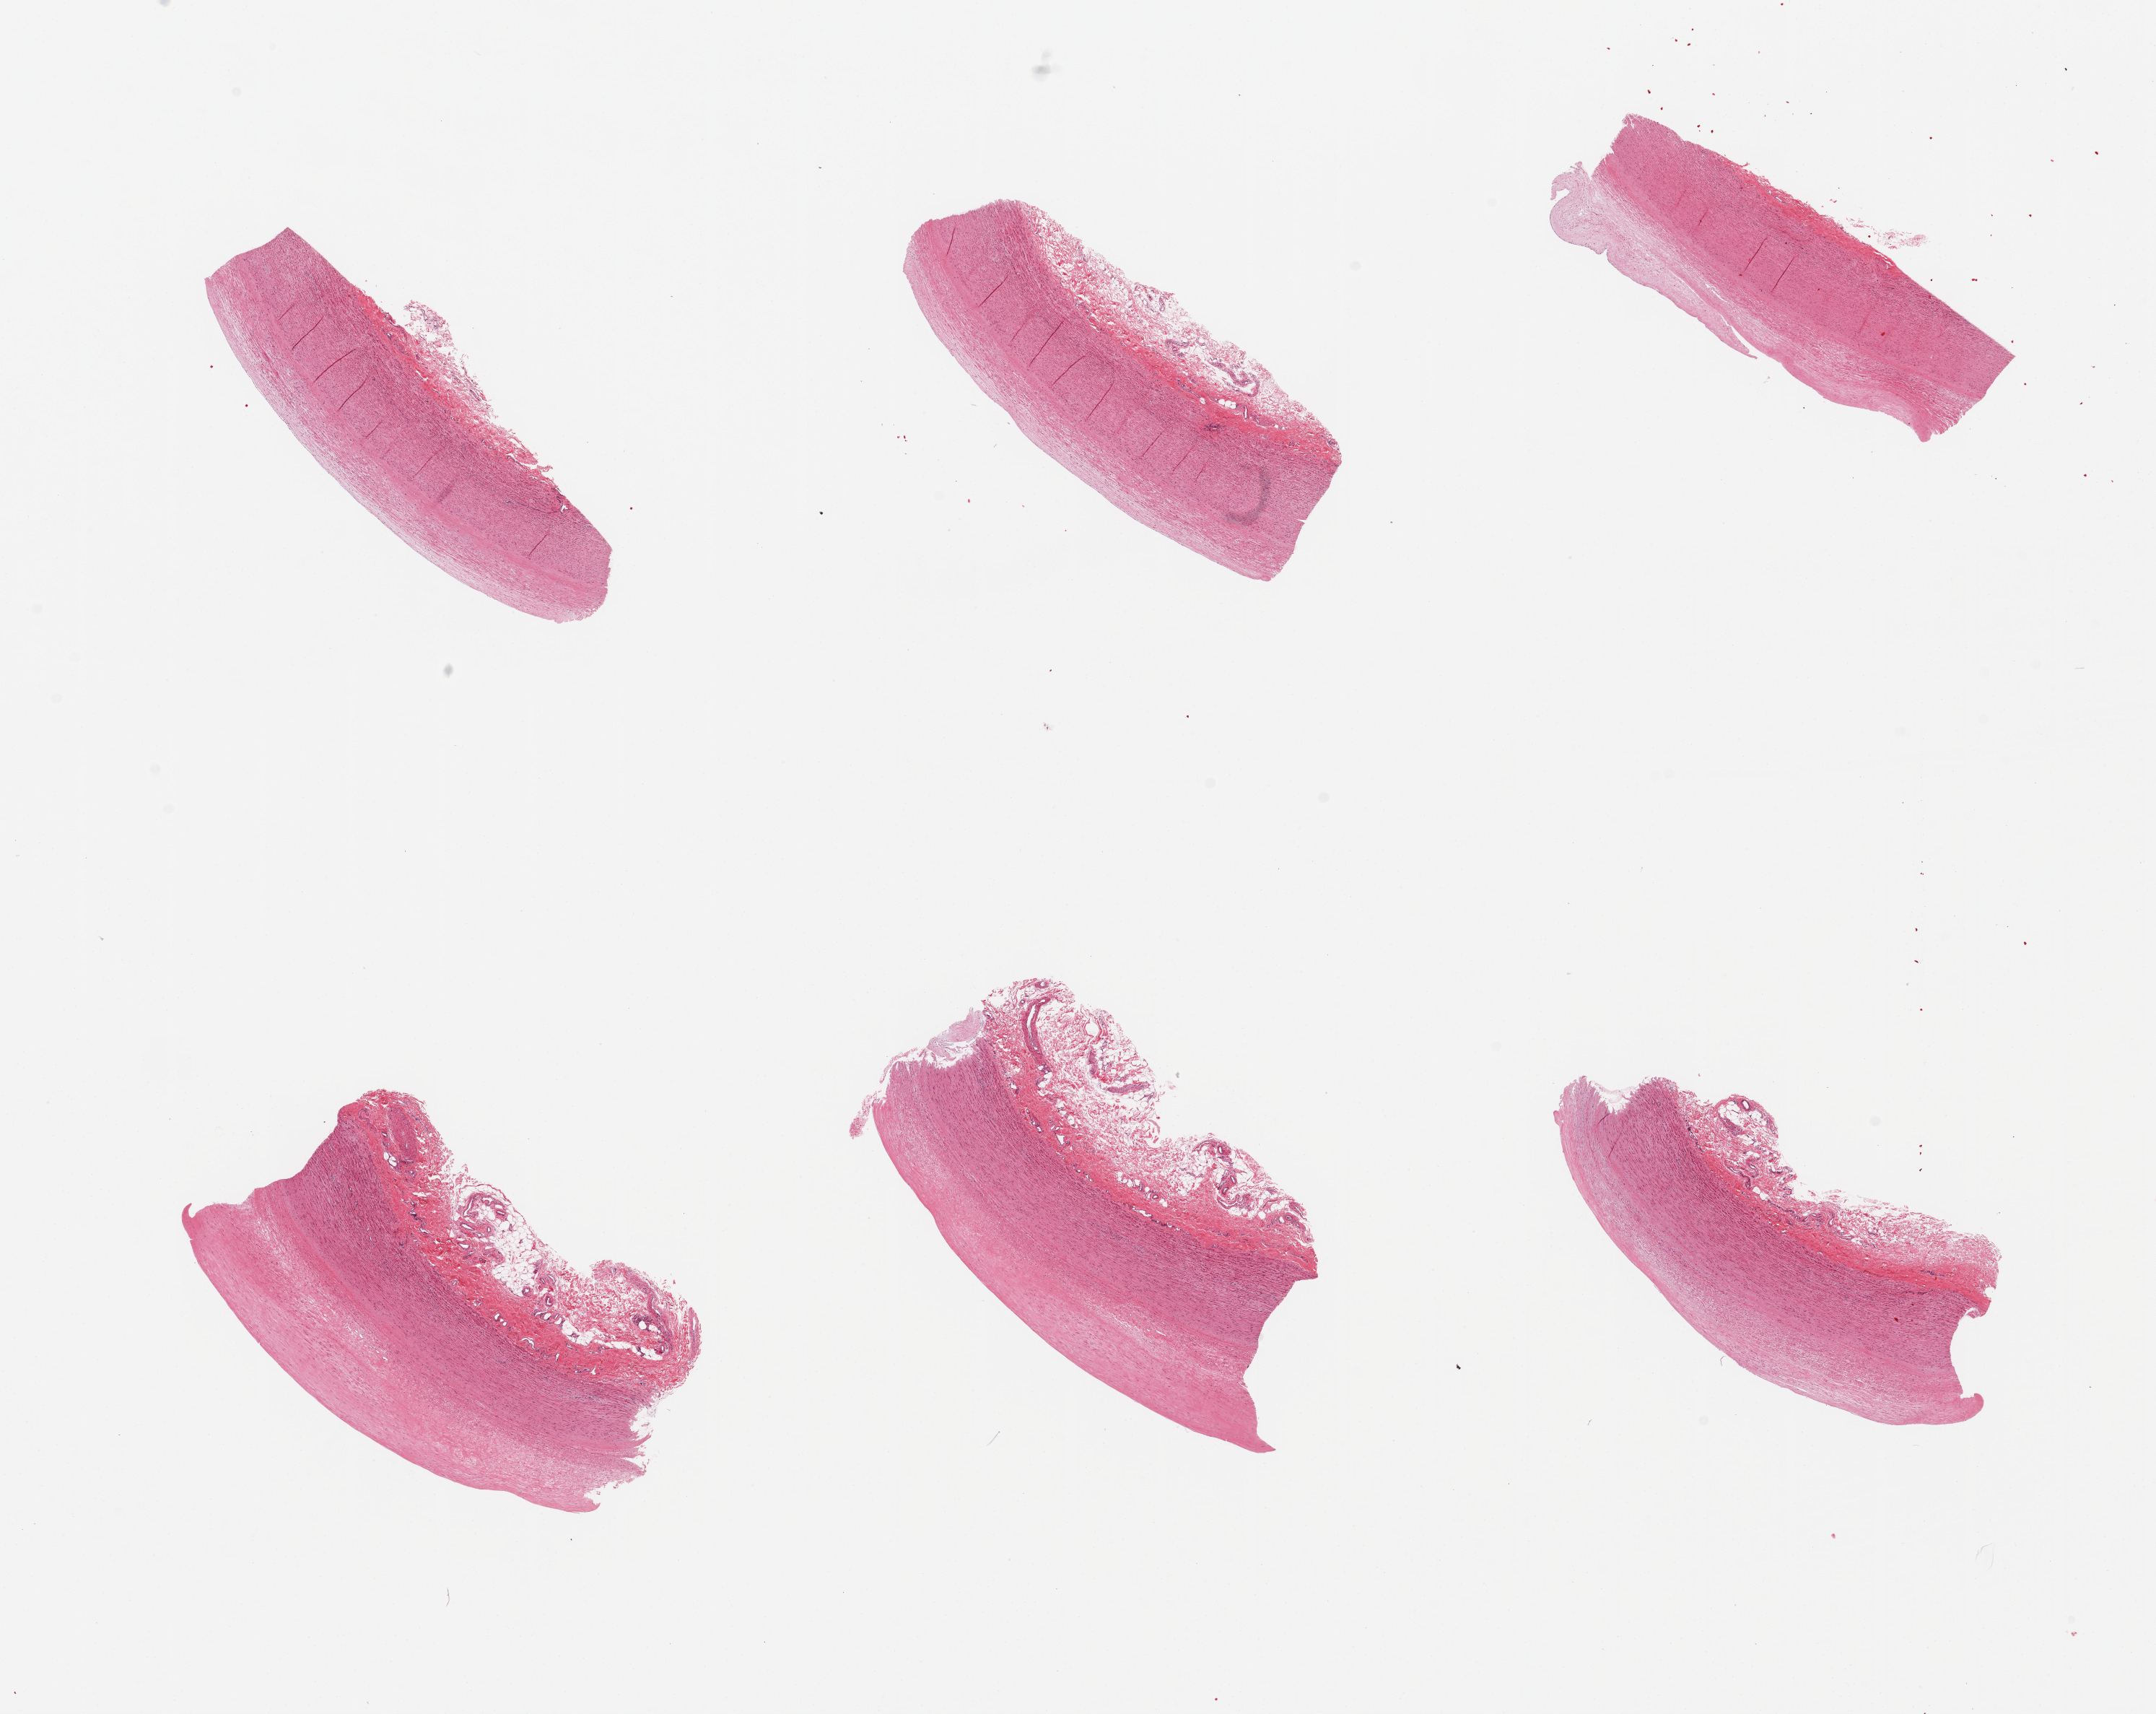
H&E whole-slide image, brightfield — a low-resolution overview of the entire scanned area, about 23.6 x 18.8 mm (acquisition: 20x scan), PAXgene-fixed paraffin-embedded (PFPE) section, target tissue: aorta, tissue donor sample. Donor sex: male.
Pathologist's review note for this sample: 6 pieces; 4 have up to 1 mm periadventitial stroma; all have flat plaques.